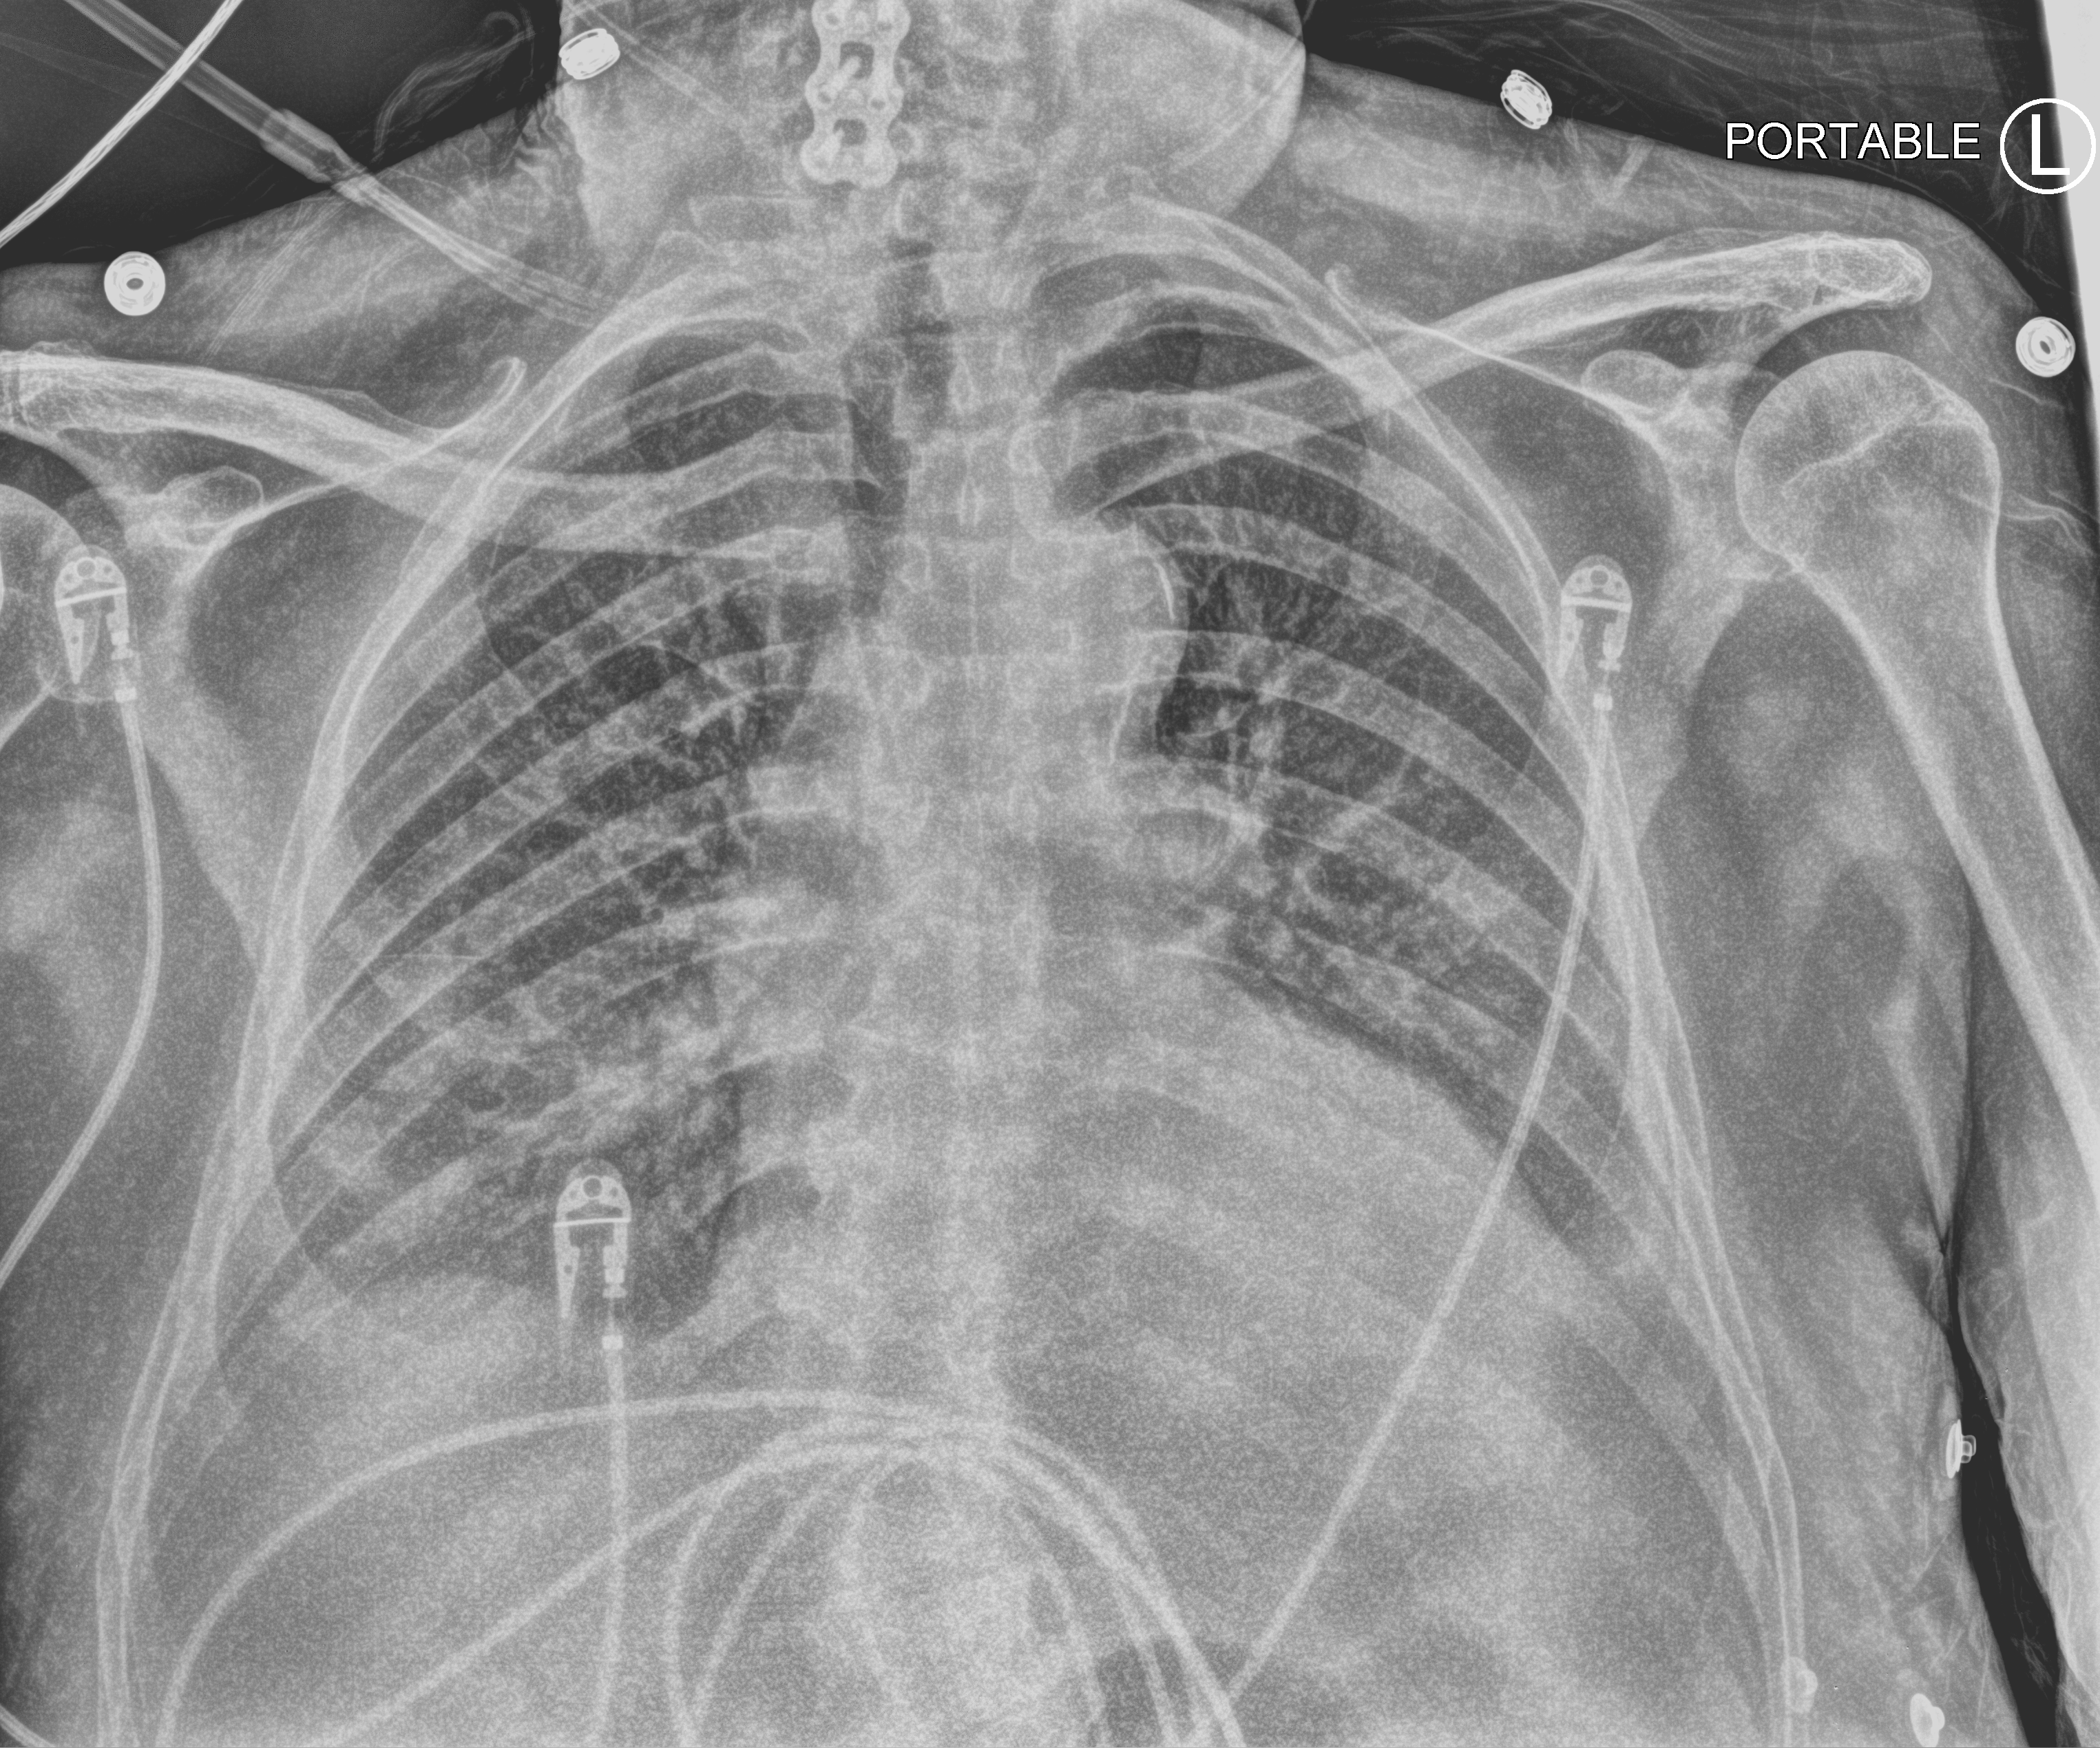
Portable chest radiograph. Male patient hospitalised with COVID-19, age 75–90 years.
Admission-level facts for this patient (not findings on this image; timing relative to this image not recorded): admitted to intensive care during this hospital stay: yes; length of hospital stay: 17 days.